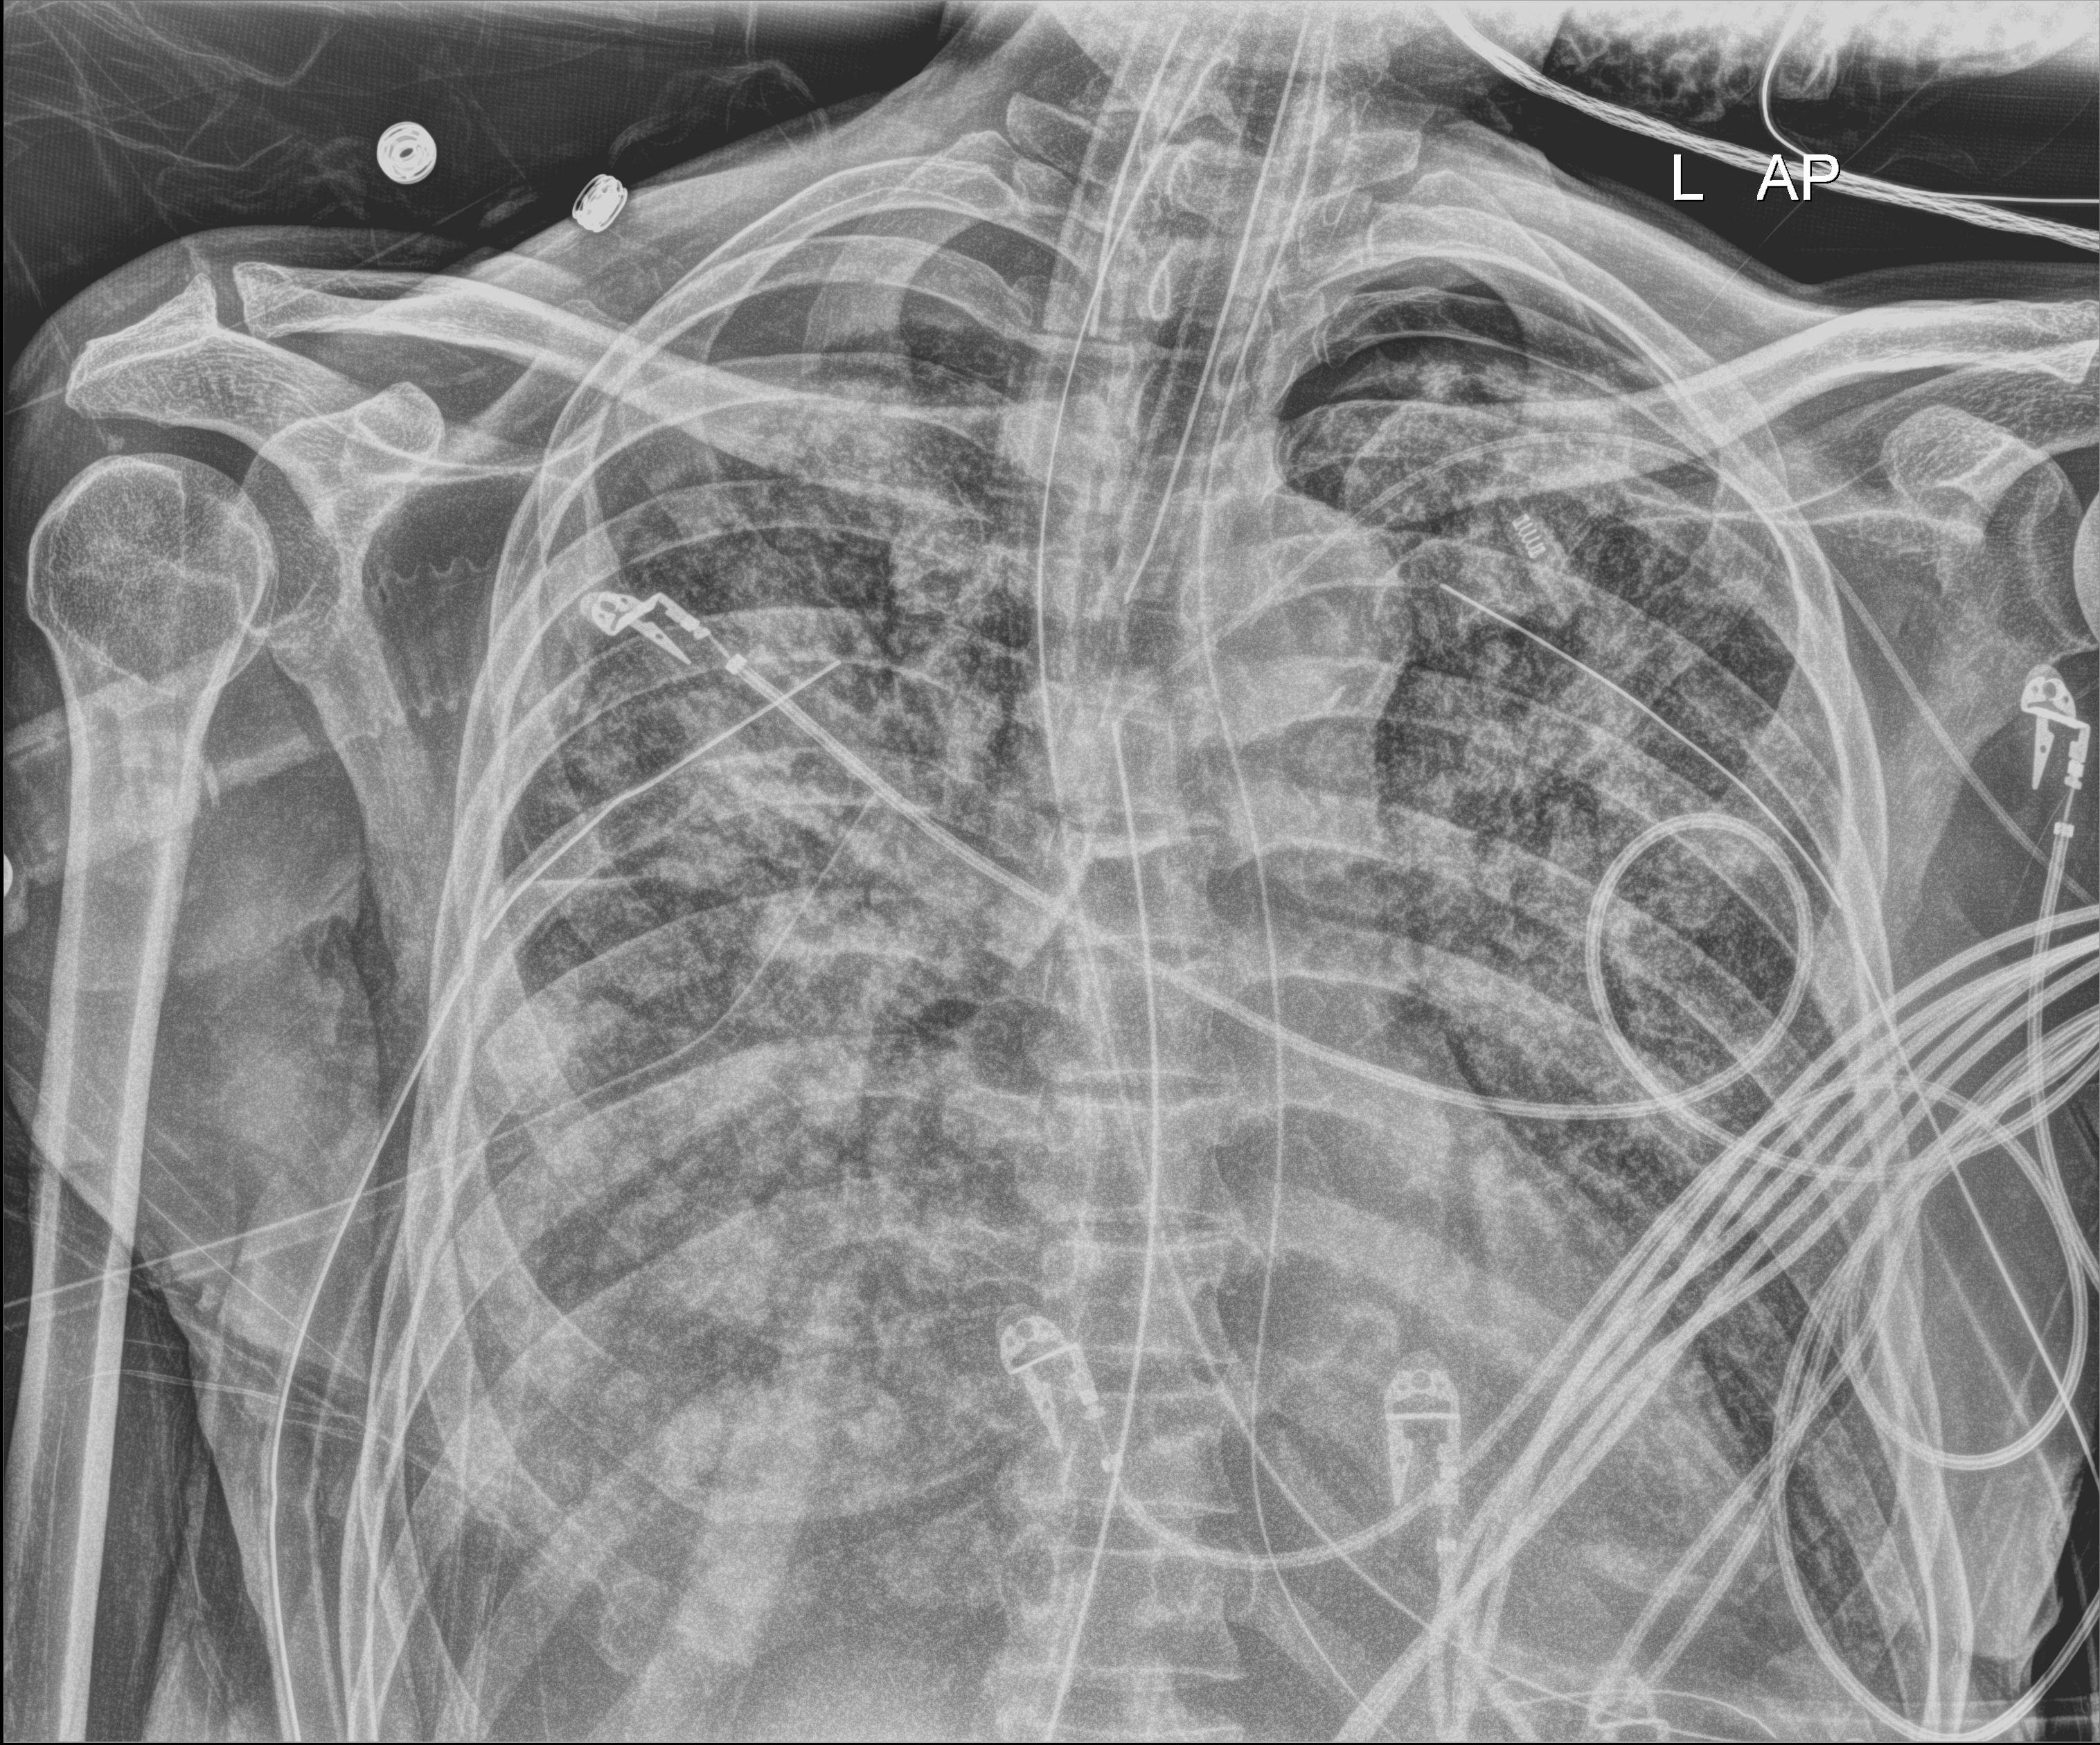
Bedside chest radiograph (digital radiography), anteroposterior (AP) projection. Patient hospitalised with COVID-19; male, aged 60–74 years.
Hospital-stay facts (about this admission, not read from this image; timing relative to this image not recorded):
- other chronic lung disease (admission record): no
- admitted to intensive care during this hospital stay: yes
- diabetes (admission record): no